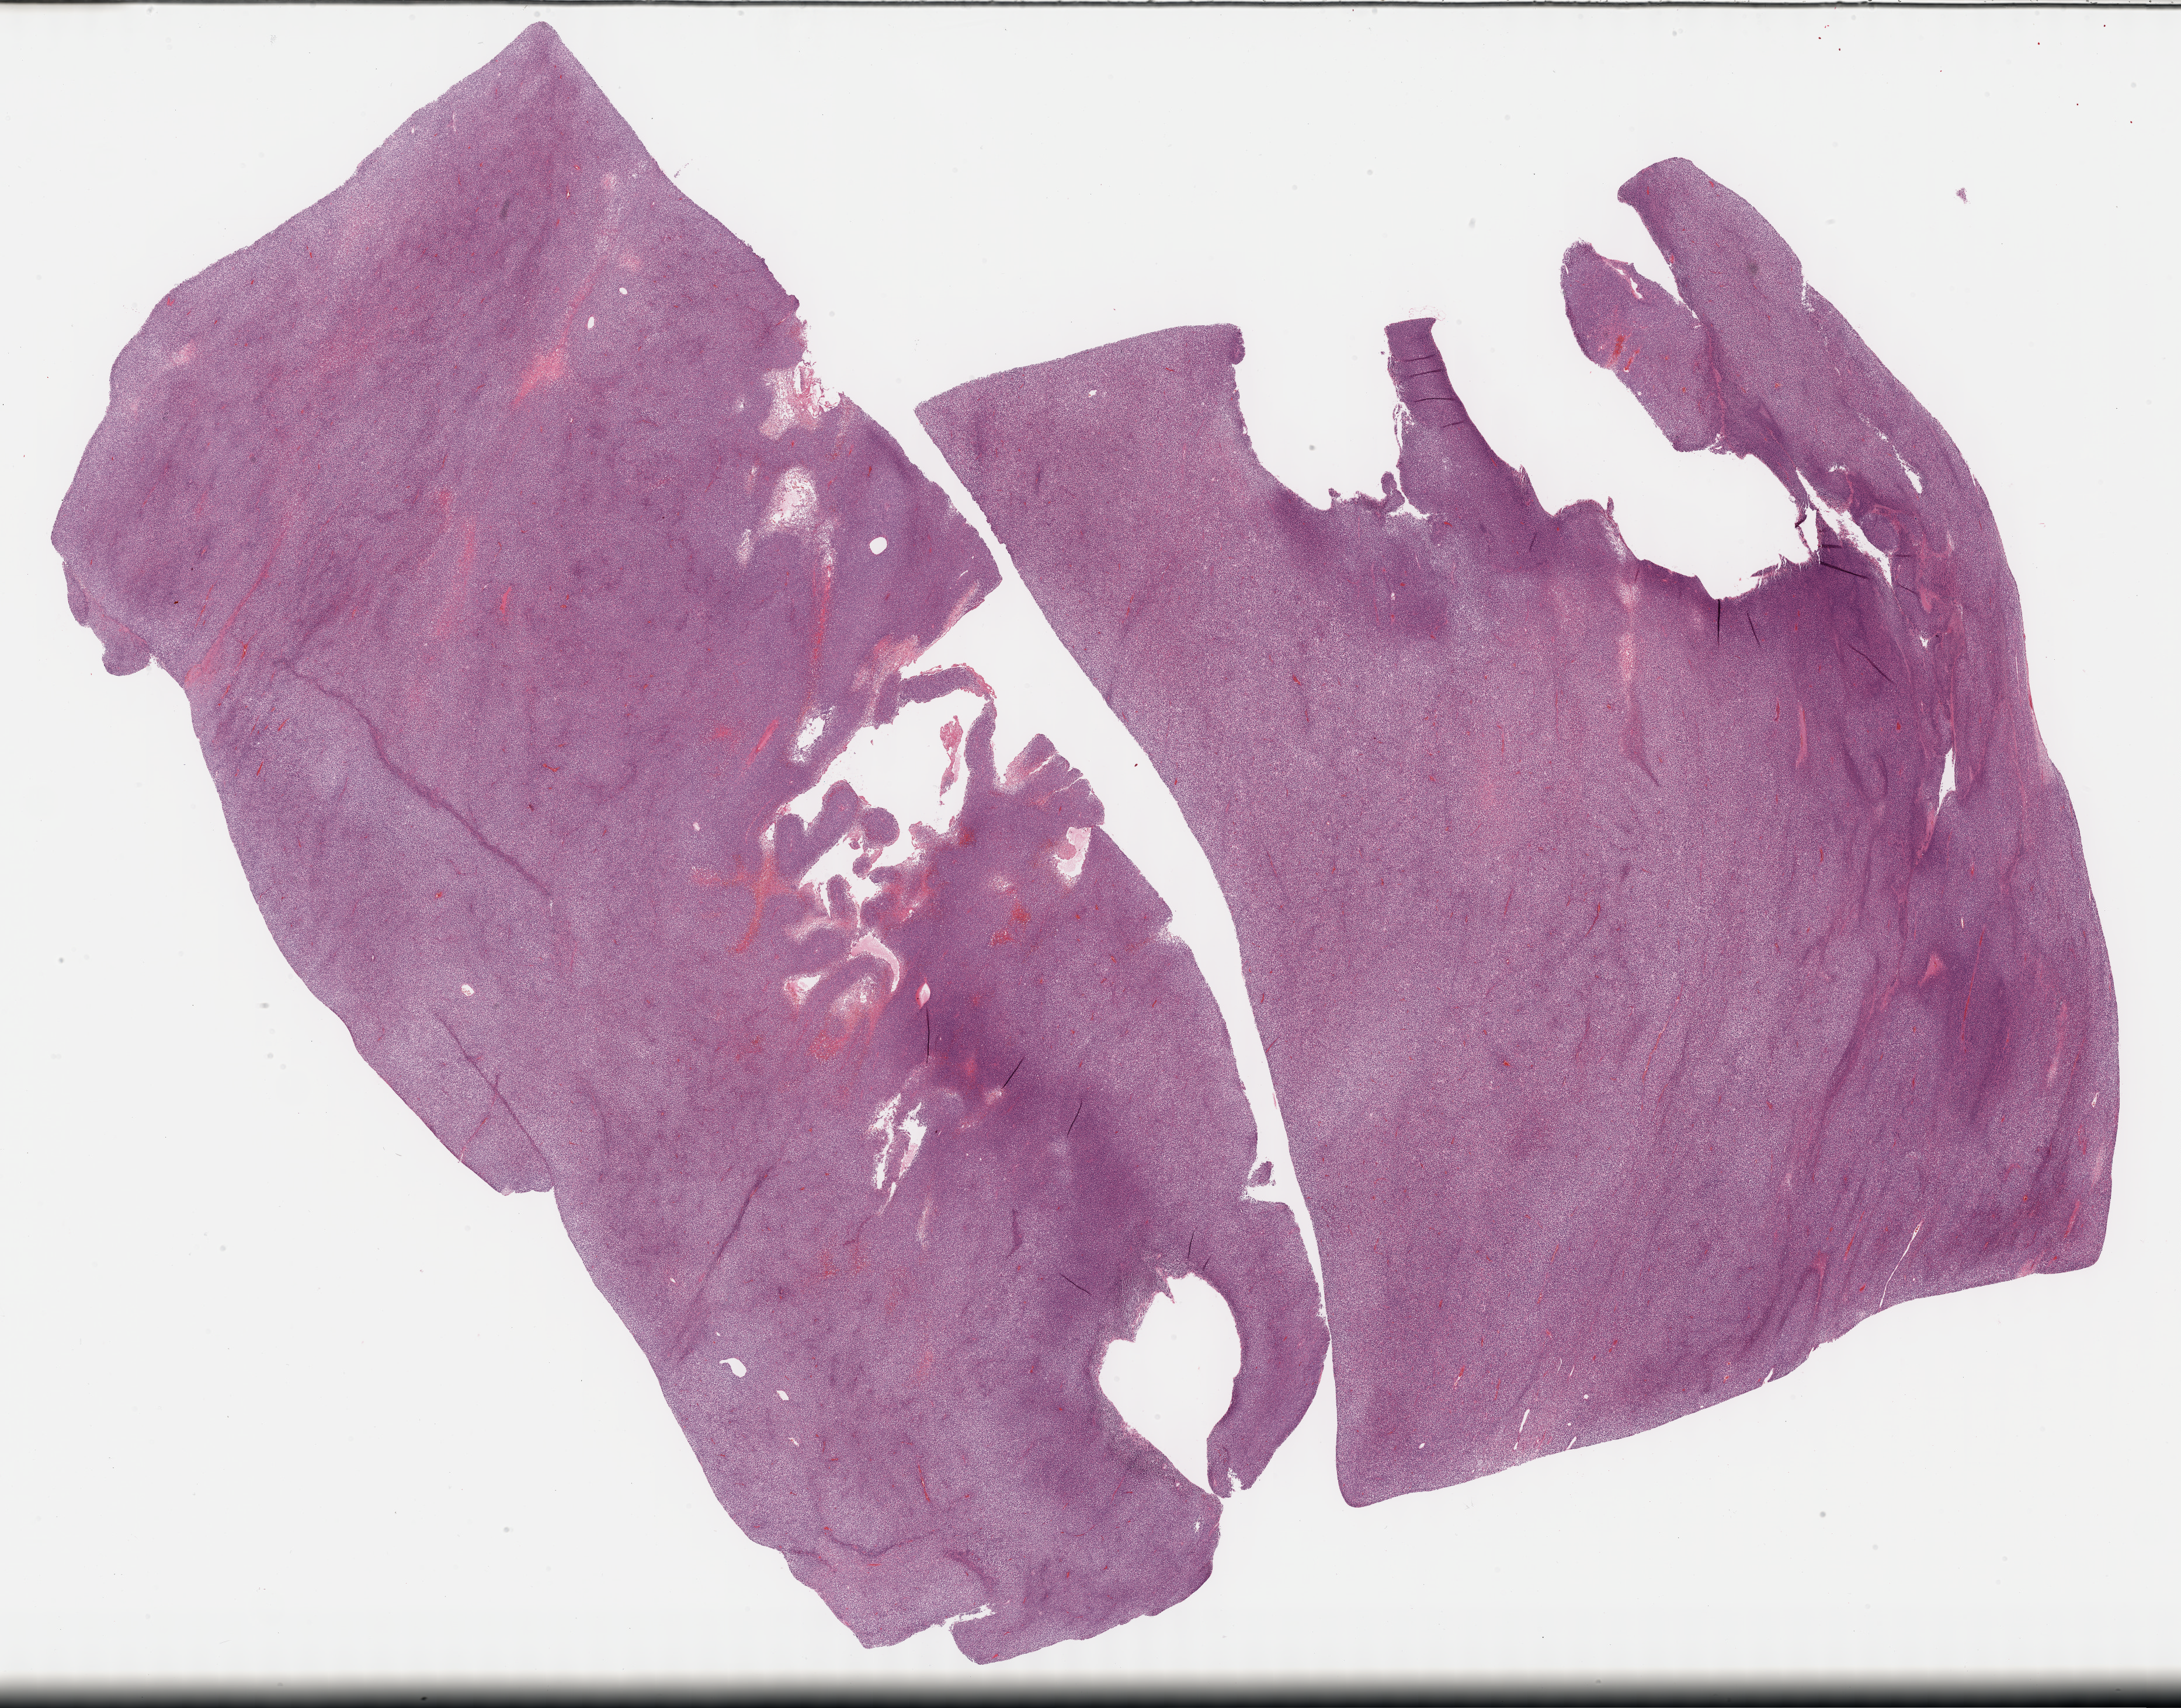
Whole-slide histology image, H&E — low-resolution overview of the scanned area, about 30.2 x 23.7 mm (acquisition: 40x scan). FFPE section. Sample: primary tumour, connective, subcutaneous and other soft tissues. Male, age 27 years at initial diagnosis.
* pathologic diagnosis: Synovial sarcoma, spindle cell (connective, subcutaneous and other soft tissues of lower limb and hip)